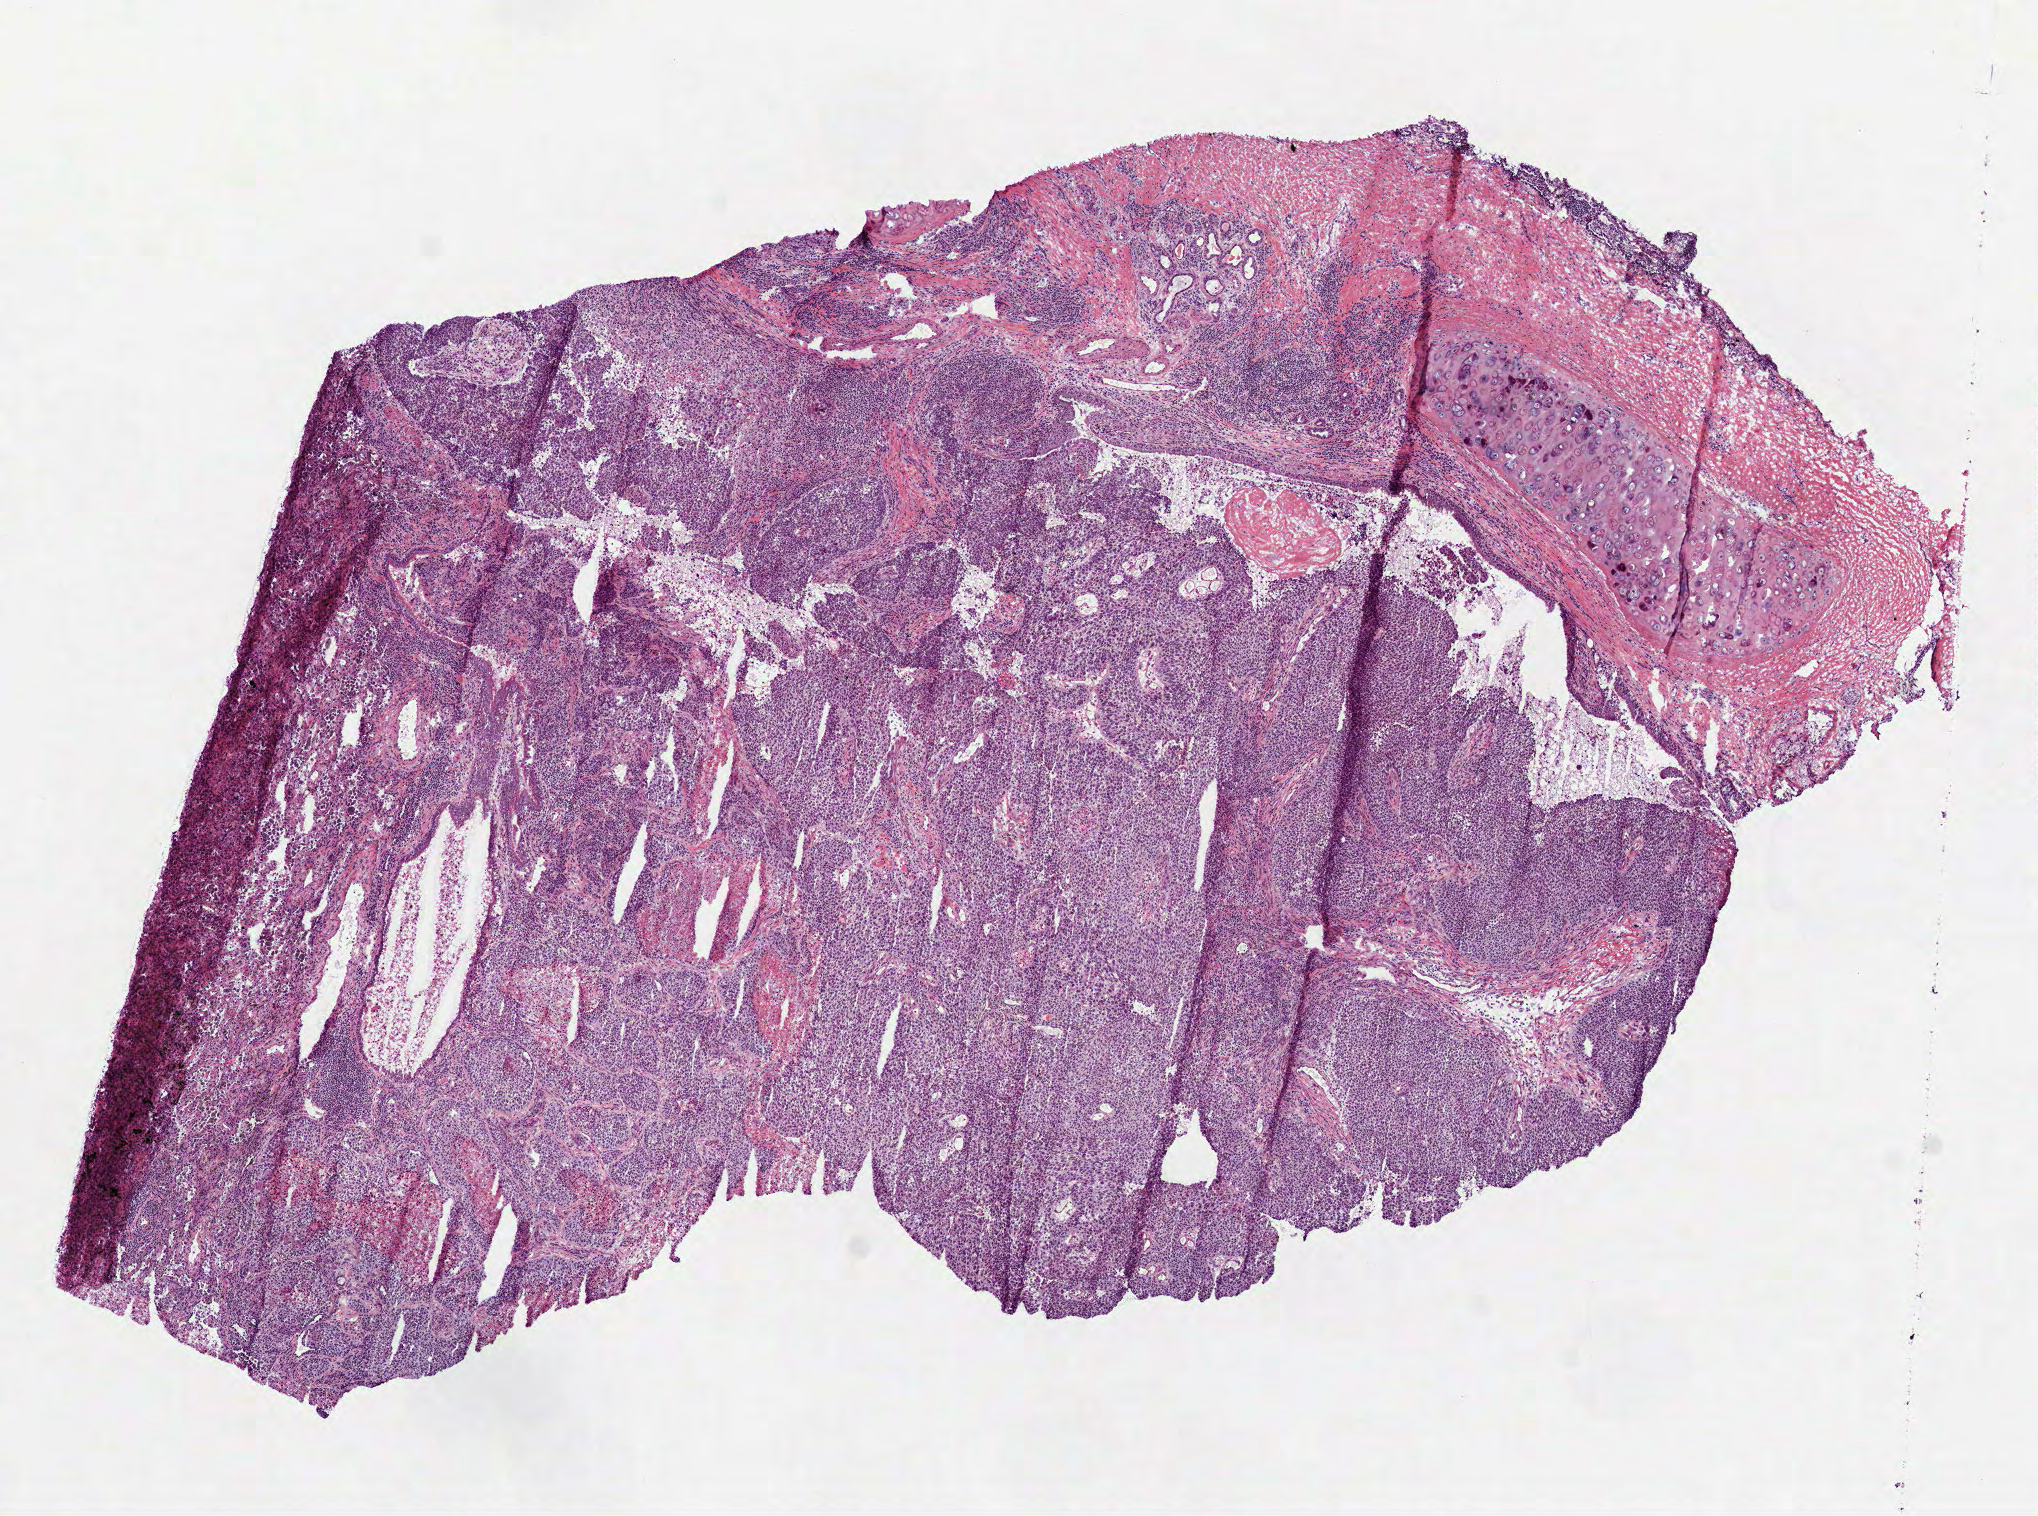
Digitized H&E-stained tissue section (whole slide) — whole scanned area (about 8.2 x 6.1 mm, acquisition: 40x scan) shown as a low-resolution overview; frozen section from the bottom of the tissue portion; lung, primary tumour sample. Patient sex: male.
Histologic diagnosis: Squamous cell carcinoma, NOS (lower lobe, lung).